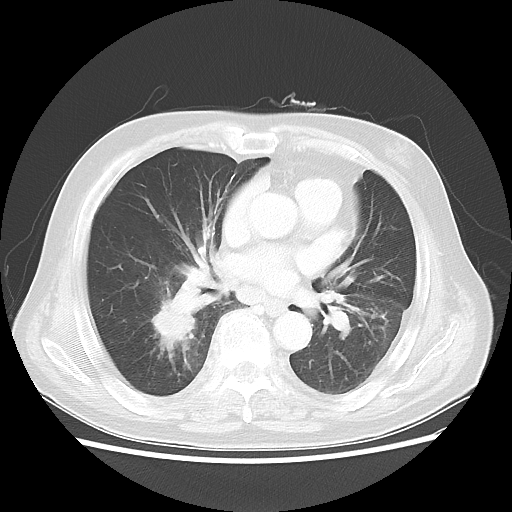
Chest CT, one axial slice; position 18 of 44 along the scan axis; reconstruction kernel LUNG; lung window (W 1500 / L -600 HU); 512 × 512 image matrix, field of view 359 × 359 mm. Patient: male, 83 years. Case-level facts recorded for this patient, not image findings: clinical TNM (as recorded): T2 N3 M0.
Annotated regions visible in this slice (bounding box drawn by a radiologist):
- lung tumour (recorded histology: adenocarcinoma): bounding box <139,294,200,353> (left, top, right, bottom; pixels)